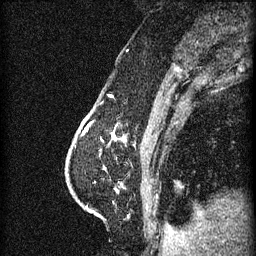
Breast MRI (dynamic contrast-enhanced), one sagittal slice. Slice 18 of 60 in the series (ordered by position). 3 images stored at this slice position (order not interpretable as contrast timing). 1.5 T. TE 4.2 ms, TR 11 ms. 1.5 mm slice thickness. 256 × 256 image matrix, field of view 180 × 180 mm. Female patient, age 63 years.
Annotated regions visible in this slice (semi-automatic segmentation, software-assisted and operator-edited):
- analysis volume of interest (the breast-tissue region the enhancement analysis was run in; not a lesion): box from (x=86, y=118) to (x=127, y=151) px
- tumour enhancement mask (voxels above the 70 % enhancement threshold inside the analysis volume of interest): (x=86, y=124)–(x=127, y=141)